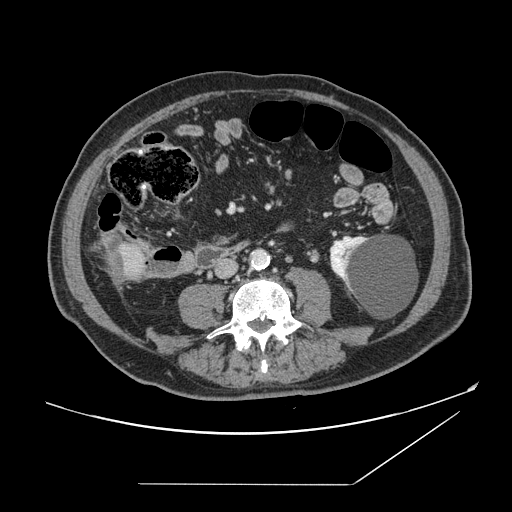
Contrast-enhanced abdominal CT, one axial slice; slice 24 of 166 in the series (ordered by position); intravenous contrast given; soft-tissue window (W 400 / L 40 HU); 2.5 mm slice thickness; 512 × 512 image matrix. Male patient, age 80 years. From the clinical record (not read from this slice): diagnosis: colorectal cancer liver metastases, imaged before liver resection; multiple liver metastases: no; largest metastasis: 2.2 cm; disease in both lobes: no.
Outlined on this slice (manually delineated by an expert):
- liver: bounding box (x1, y1, x2, y2) in pixels: (104, 238, 149, 283)
- liver metastasis: (108, 246, 131, 281)